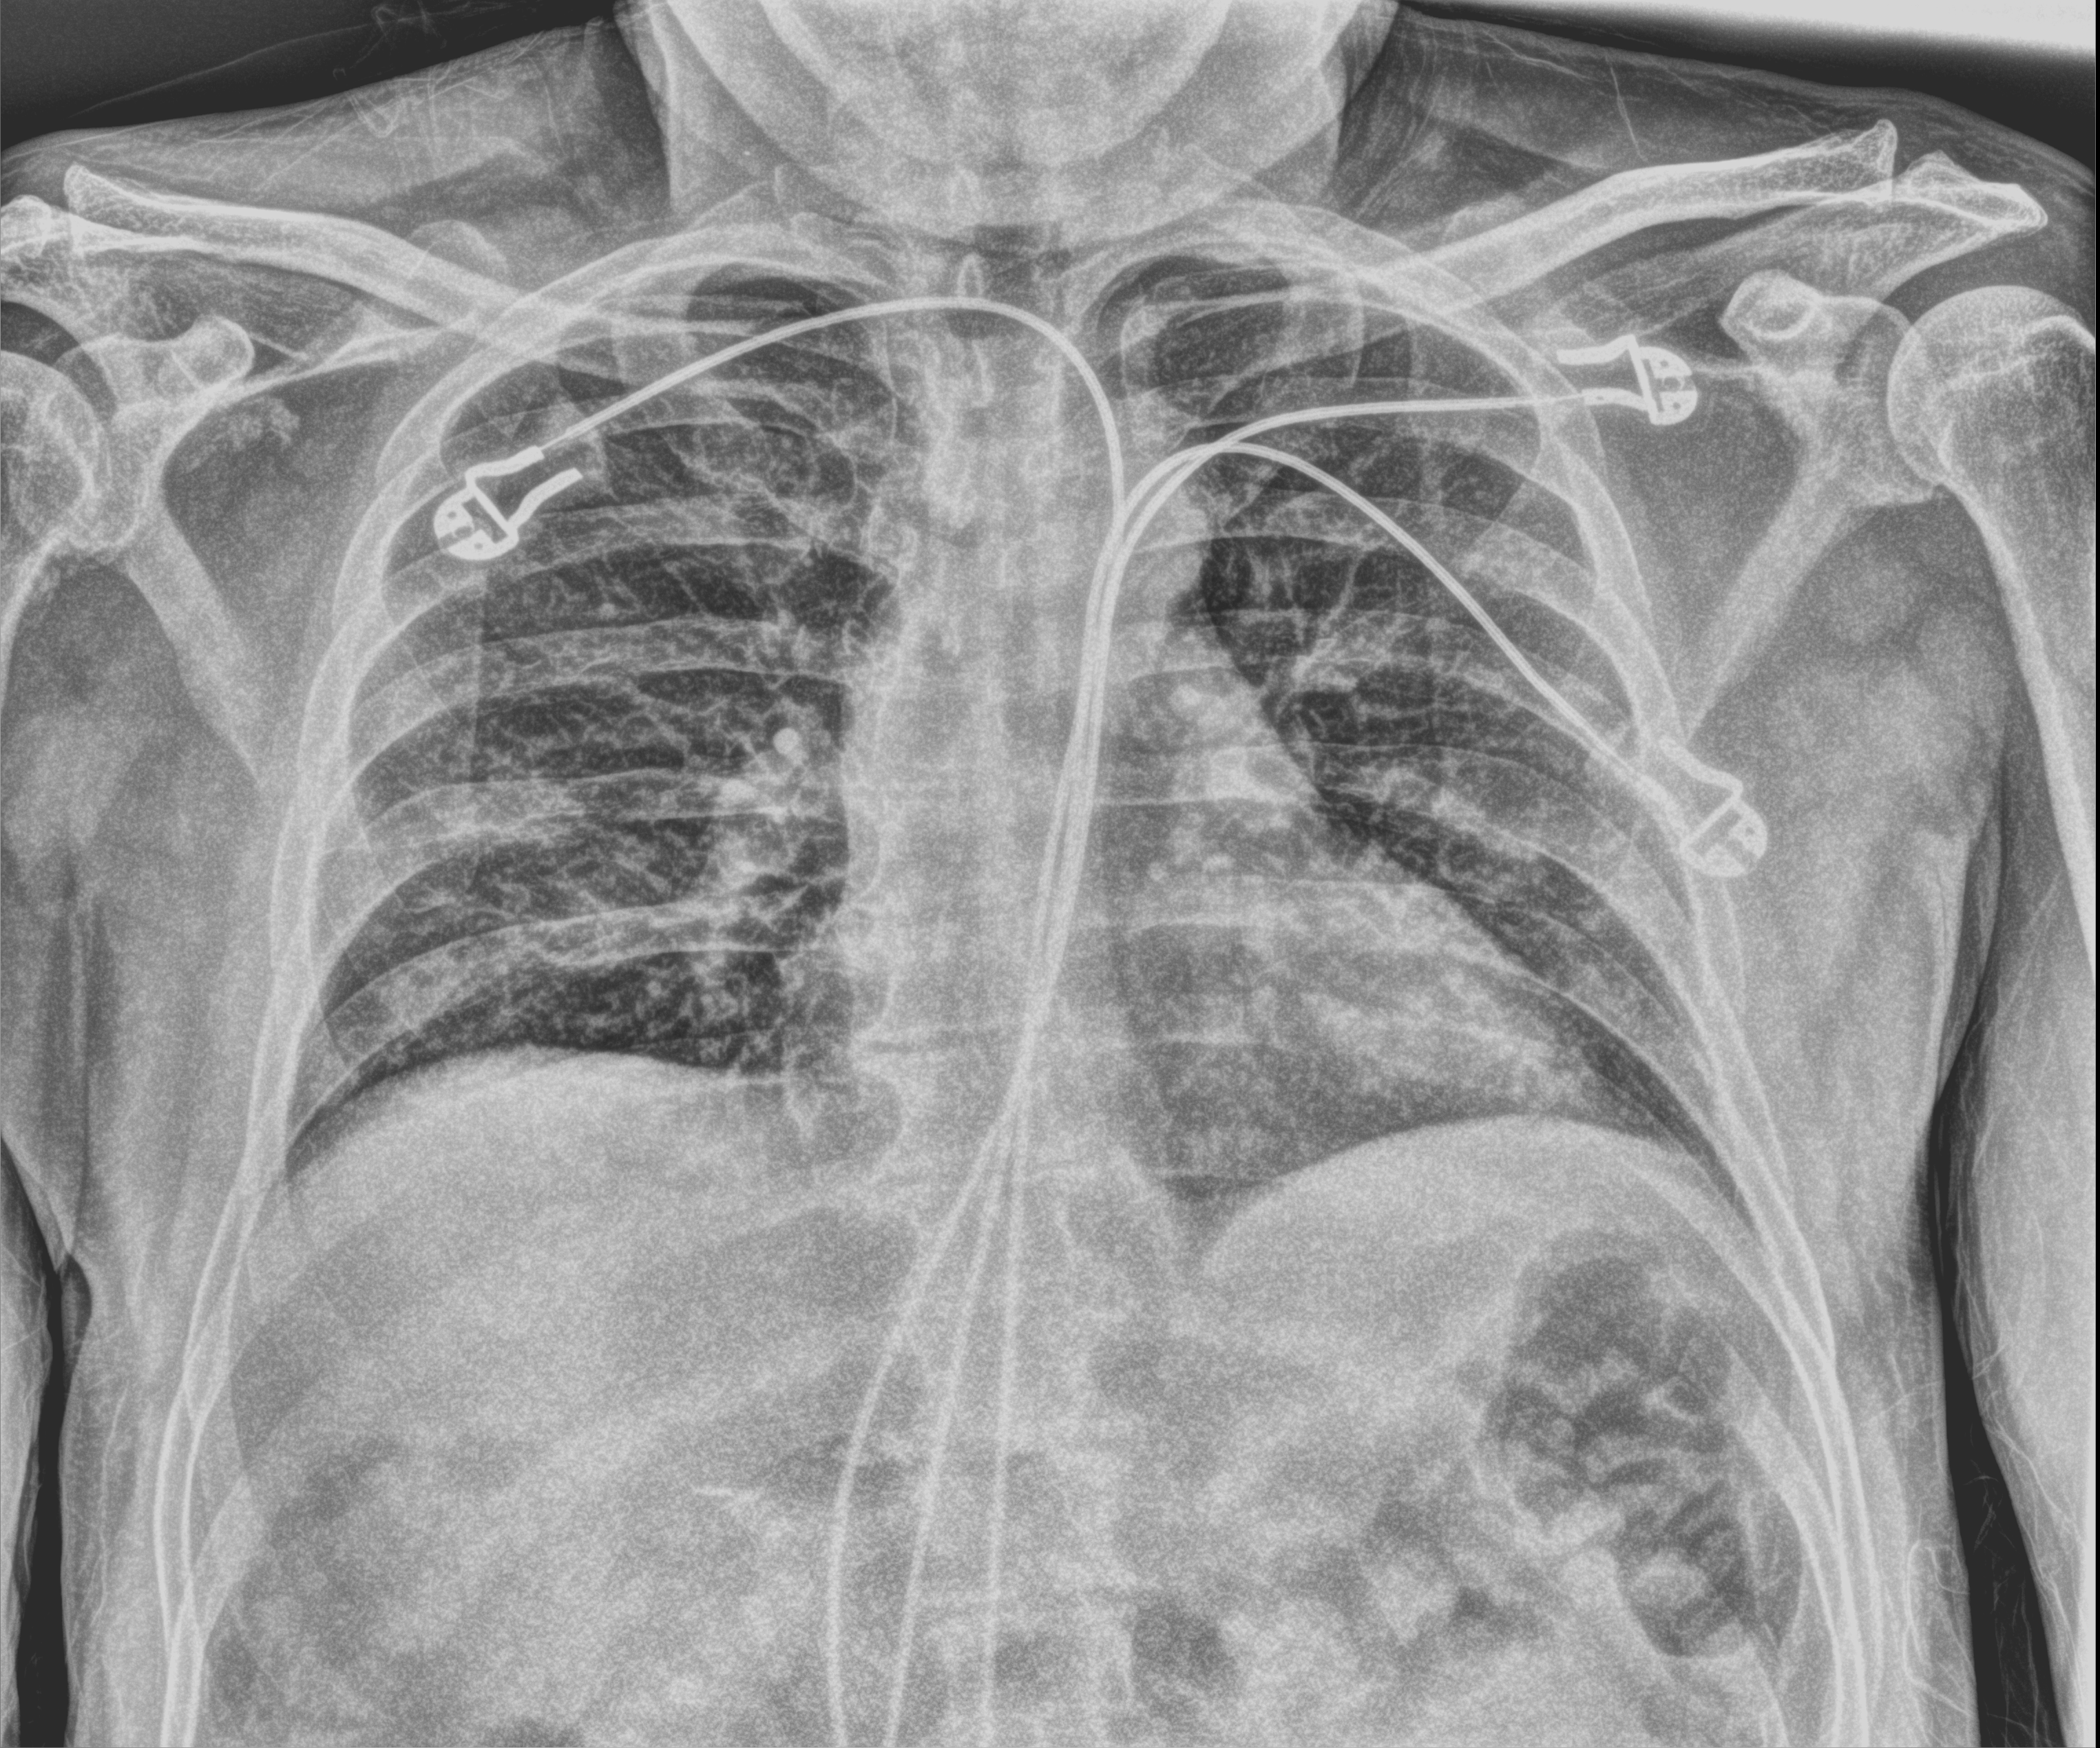
Portable chest radiograph, anteroposterior (AP) projection. Male patient hospitalised with COVID-19, age 18–59 years.
From the hospital-stay record, not from the radiograph (when in the stay this image was taken is not recorded):
- length of hospital stay: 13 days
- mechanically ventilated during this hospital stay: no
- admitted to intensive care during this hospital stay: no